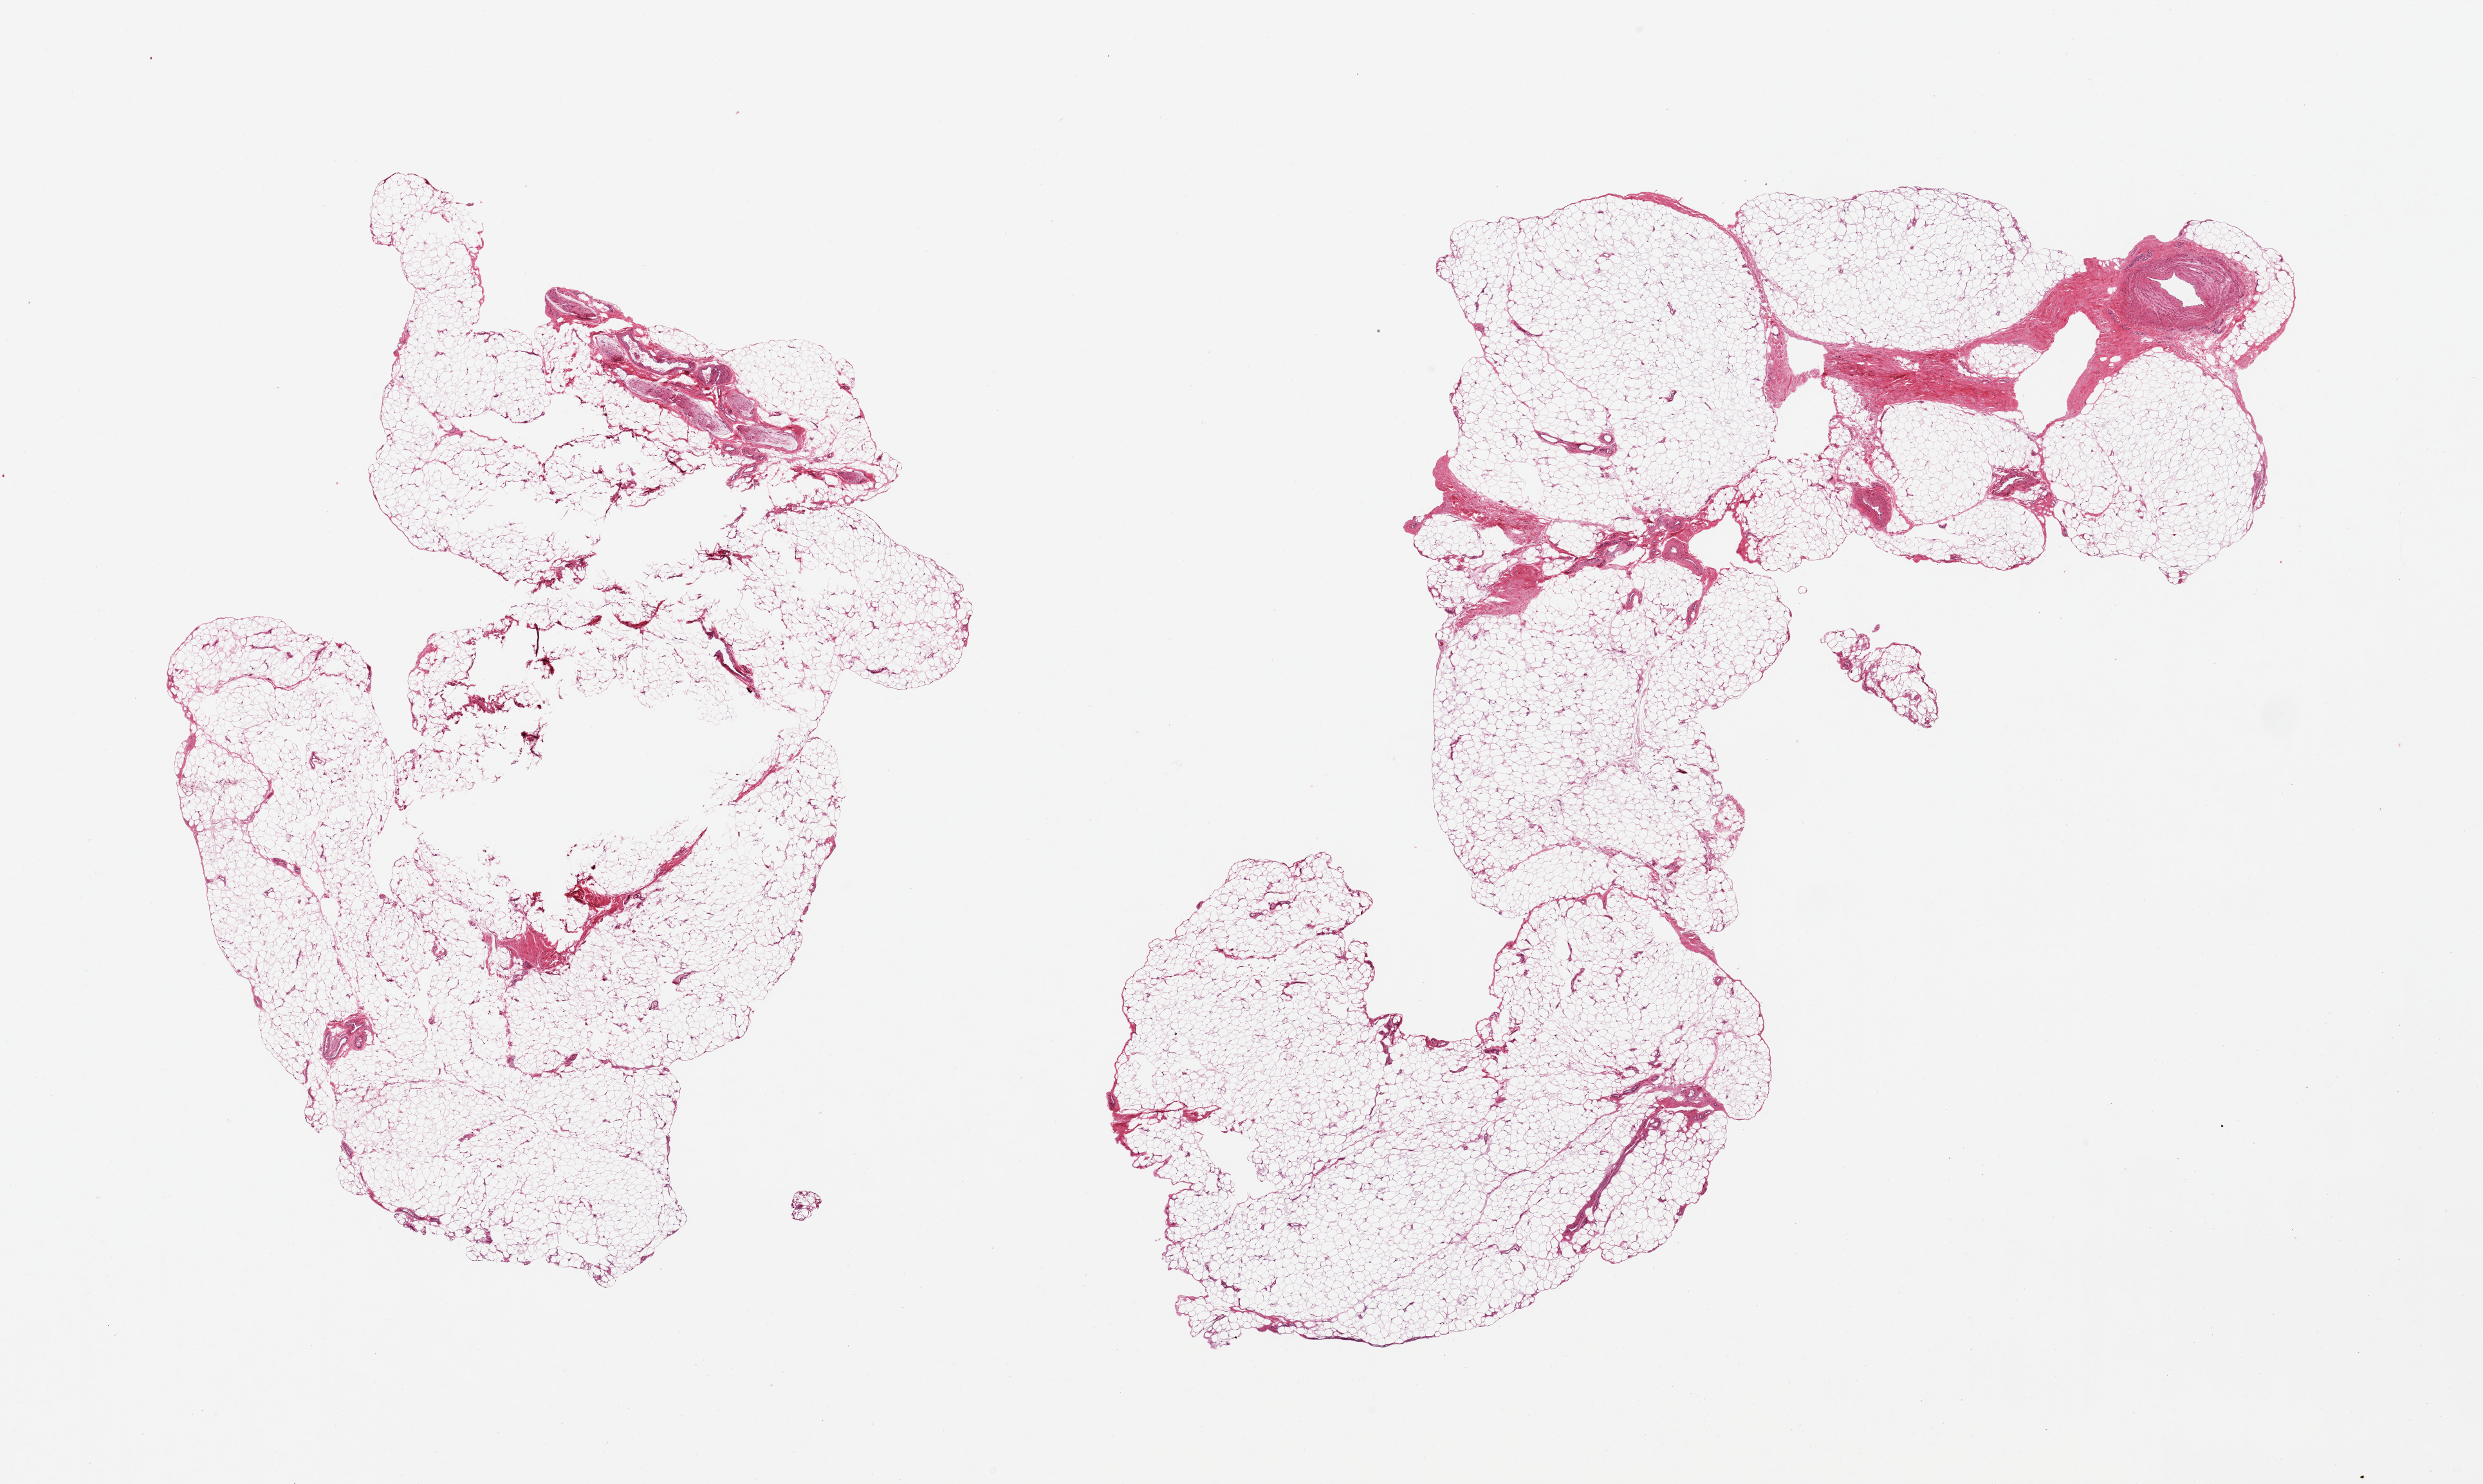
Haematoxylin and eosin whole-slide image, brightfield, a low-resolution overview of the entire scanned area, about 30.5 x 18.2 mm (acquisition: 20x scan); PAXgene-fixed paraffin-embedded (PFPE) section; target tissue: adipose tissue; tissue donor sample.
Pathologist's review note for this sample: 2 pieces, ~10-15% fascia, vascular, peripheral nerve elements.